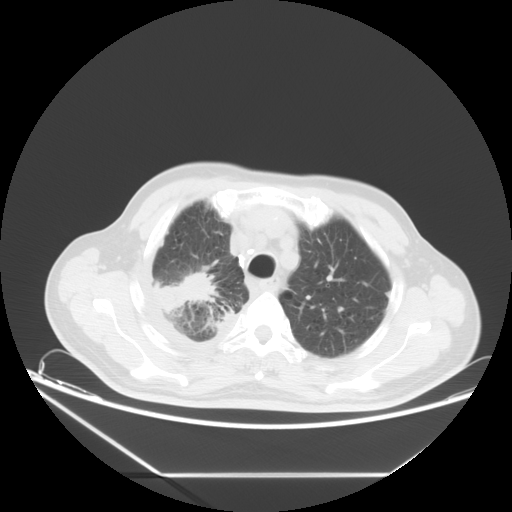
Chest CT, one axial slice. Slice 13 of 16 in the series (ordered by position). Lung window (W 1500 / L -600 HU). 5 mm slice thickness. 512 × 512 image matrix, field of view 418 × 418 mm. Patient: male, 75 years. From the clinical record (not read from this slice): clinical TNM (as recorded): T1c N1 M1.
Outlined on this slice (rectangle marked by the reading radiologist):
- lung tumour (recorded histology: adenocarcinoma): bounding box (x1, y1, x2, y2) in pixels: (145, 264, 223, 311)